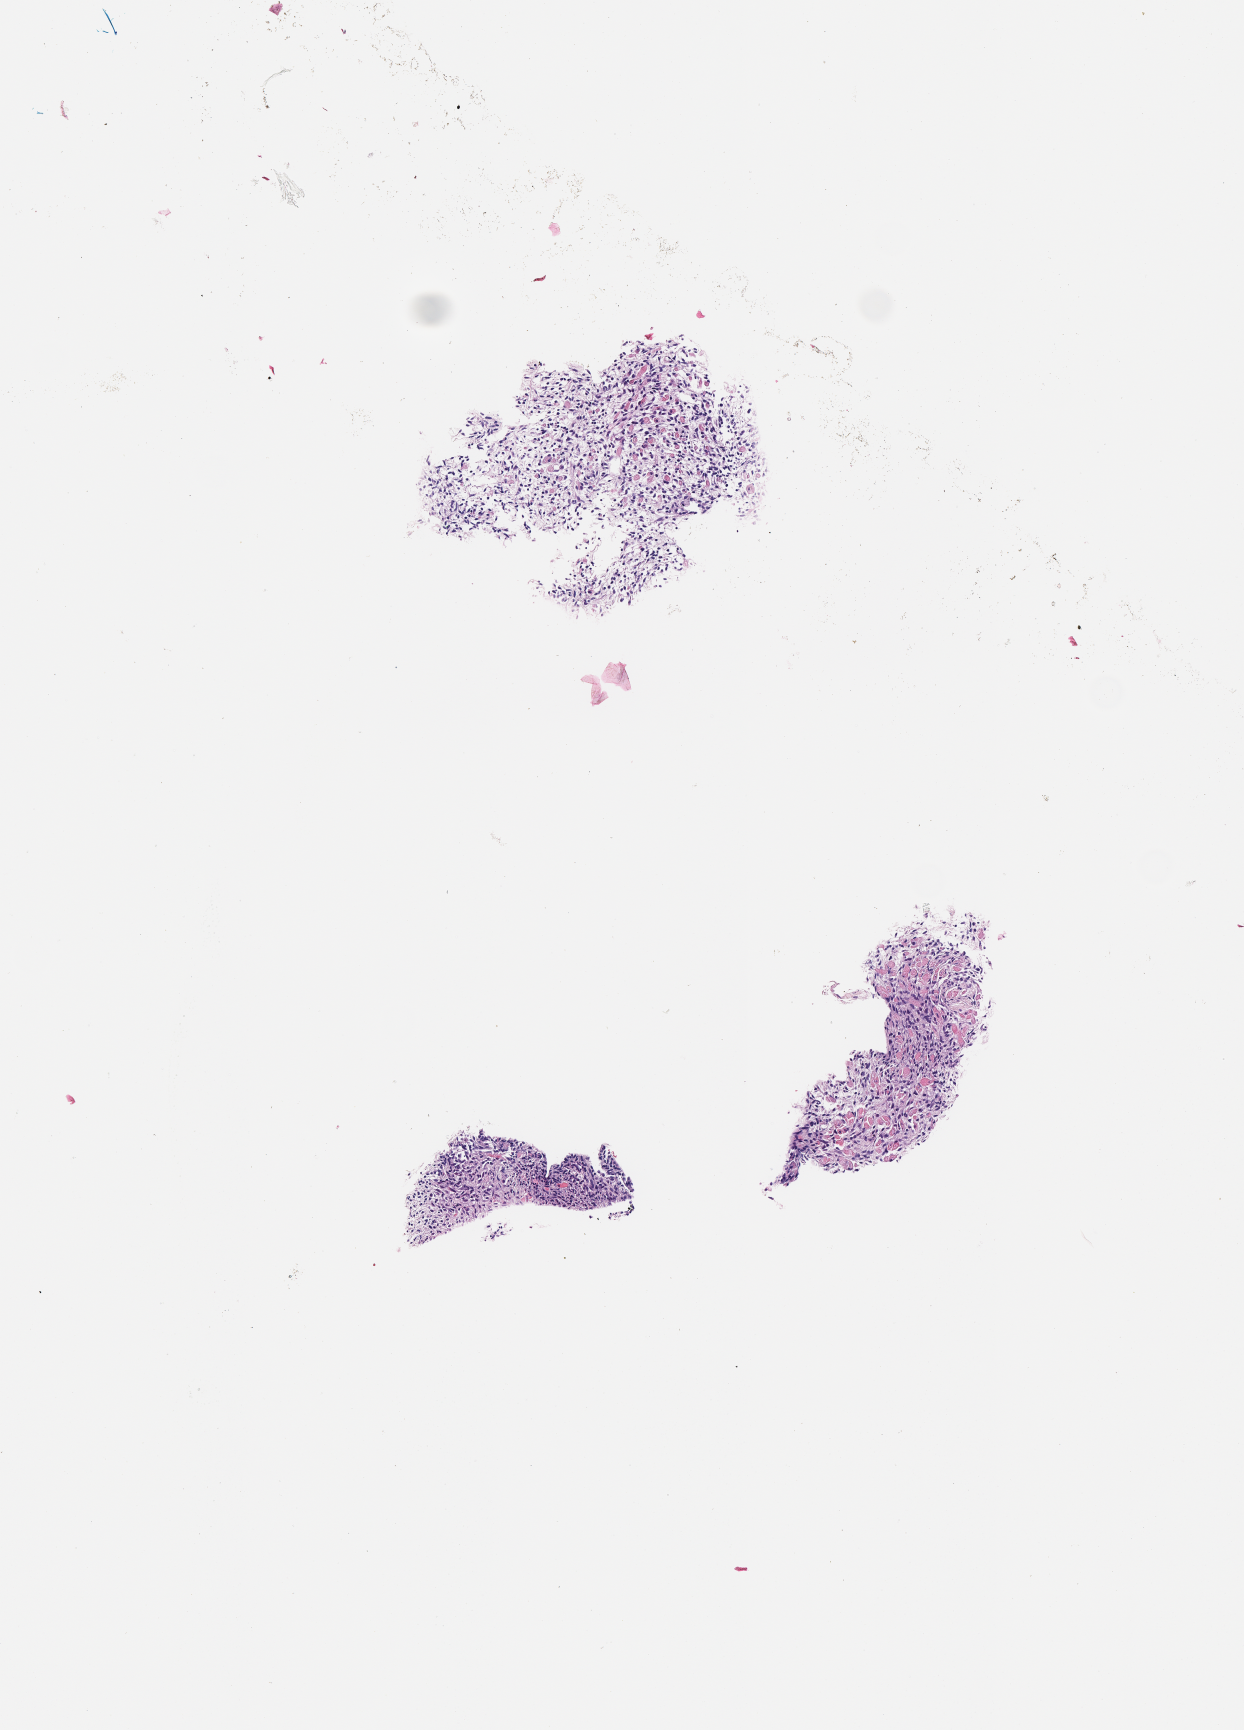
Hematoxylin and eosin (H&E) whole-slide image of tumor tissue, whole scanned area (about 2.5 x 3.5 mm) shown as a low-resolution overview, FFPE section, site: leg. Female patient, age at diagnosis 44.6 years.
Metastatic status at presentation (as recorded): non-metastatic (confirmed). Diagnosis: rhabdomyosarcoma. Stage (as recorded): 3.